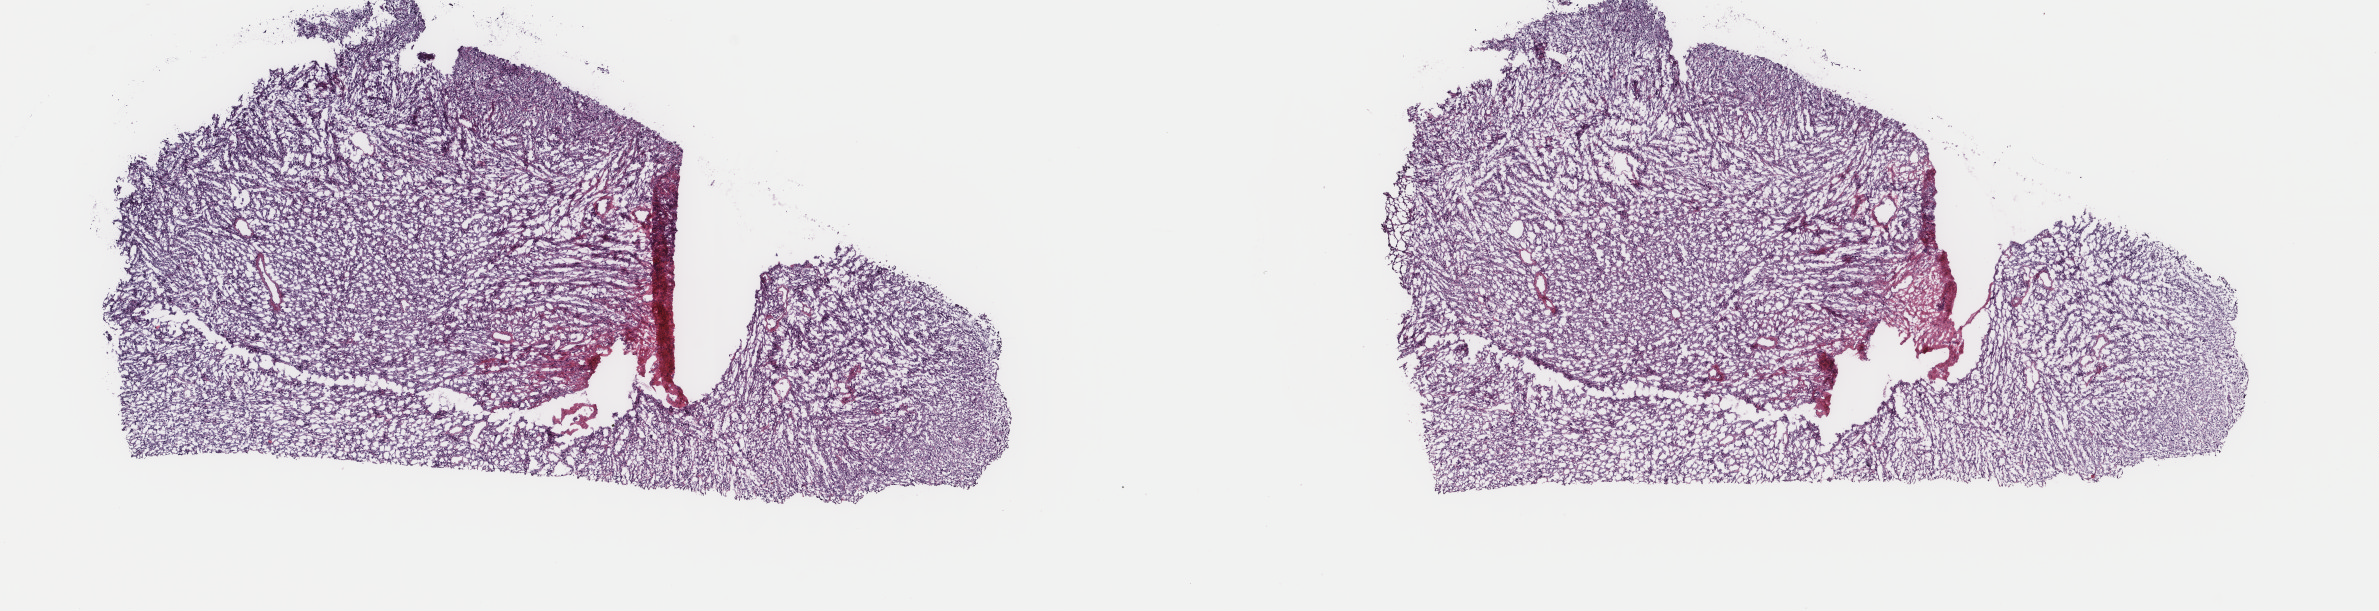
Digitized H&E tissue section (whole slide), whole scanned area (about 18.9 x 4.9 mm, acquisition: 40x scan) shown as a low-resolution overview. Frozen section. Sample: primary tumour, uterus. Patient: female, age at initial diagnosis 41 years. Composition of this section per pathologist review: tumour cells 85%, tumour nuclei 100%, normal cells 0%, stromal cells 15%, necrosis 0%. Infiltration values recorded for this section: lymphocyte infiltration 0%, monocyte infiltration 0%, neutrophil infiltration 0%.
• histologic diagnosis: Leiomyosarcoma, NOS